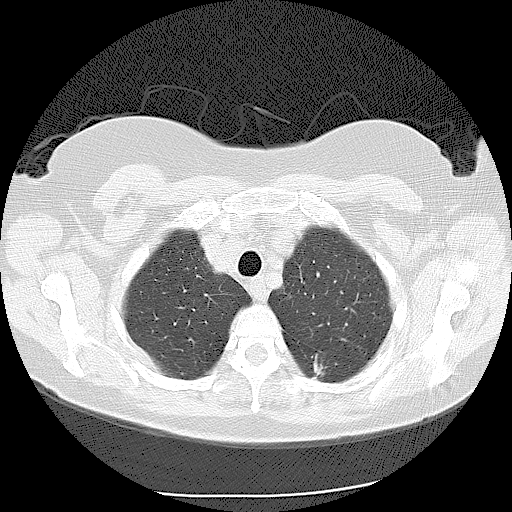
Low-dose screening chest CT, one axial slice; slice 94 of 116 in the series (ordered by position); reconstruction kernel LUNG; lung window (W 1500 / L -600 HU); 2.5 mm slice thickness; 512 × 512 image matrix, field of view 360 × 360 mm.
Outlined on this slice (outlined manually by an expert reader):
- lesion 1 (tumor, lower lobe of left lung): bounding box [x1, y1, x2, y2] px = [313, 354, 325, 376]